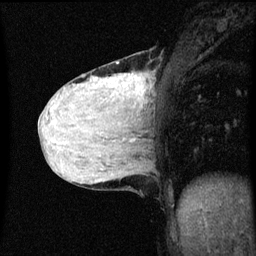
Breast MRI (dynamic contrast-enhanced), one sagittal slice; slice 23 of 60 in the series (ordered by position); dynamic contrast-enhanced series, image 2 of 3 at this slice position (ordered by acquisition); 1.5 T; TE 4.2 ms, TR 8.4 ms; 2 mm slice thickness; 256 × 256 image matrix. Female patient, age 36 years.
Annotated regions visible in this slice (semi-automatic segmentation, software-assisted and operator-edited):
- analysis volume of interest (the breast-tissue region the enhancement analysis was run in; not a lesion): bounding box <48,52,157,151> (left, top, right, bottom; pixels)
- tumour enhancement mask (voxels above the 70 % enhancement threshold inside the analysis volume of interest): <138,80,145,87>